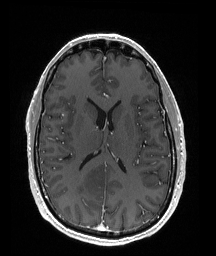
Brain MRI from a brain-tumour surgery series, one axial slice; position 82 of 176 along the scan axis; T1-weighted post-contrast; 1 mm slice thickness; 216 × 256 image matrix, field of view 211 × 250 mm. From the clinical record (not read from this slice): histopathology: Oligodendroglioma; WHO grade: 2; IDH mutation: yes; tumour location: Right Parietal.
Outlined on this slice (expert manual segmentation):
- tumour: box from (x=70, y=165) to (x=111, y=197) px